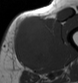
MRI of an extremity soft-tissue mass, one axial slice. Slice 18 of 43 in the series (ordered by position). MR volume resampled by the dataset authors to the PET/CT grid (not the native acquisition matrix). 78 × 83 image matrix, field of view 76 × 81 mm. Male patient. From the clinical record (not read from this slice): histological type: pleiomorphic leiomyosarcoma; grade: high; site of the primary tumour: left thigh.
Annotated regions visible in this slice (expert contour drawn on MRI and transferred to this co-registered scan by the dataset authors):
- gross tumour volume including surrounding oedema: bounding box (x1, y1, x2, y2) in pixels: (11, 17, 60, 68)
- gross tumour volume (mass): (11, 17, 55, 68)